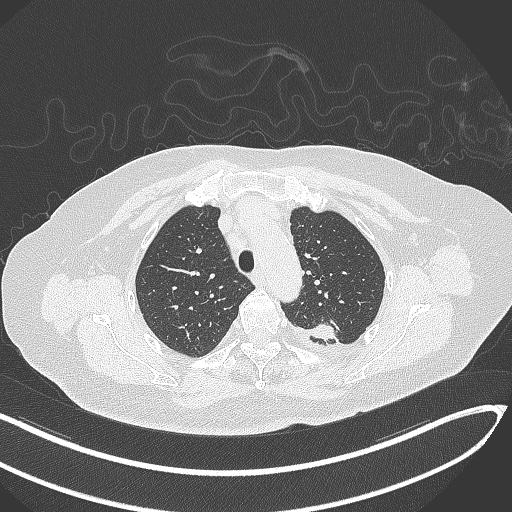
Chest CT, one axial slice. Position 248 of 270 along the scan axis. Reconstruction kernel B70f. 120 kVp. Lung window (W 1500 / L -600 HU). 1 mm slice thickness. 512 × 512 image matrix, field of view 400 × 400 mm. Patient: female, 76 years. Case-level facts recorded for this patient, not image findings: clinical TNM (as recorded): T1c N0 M0.
Annotated regions visible in this slice (bounding box drawn by a radiologist):
- lung tumour (recorded histology: adenocarcinoma): box from (x=309, y=318) to (x=336, y=342) px